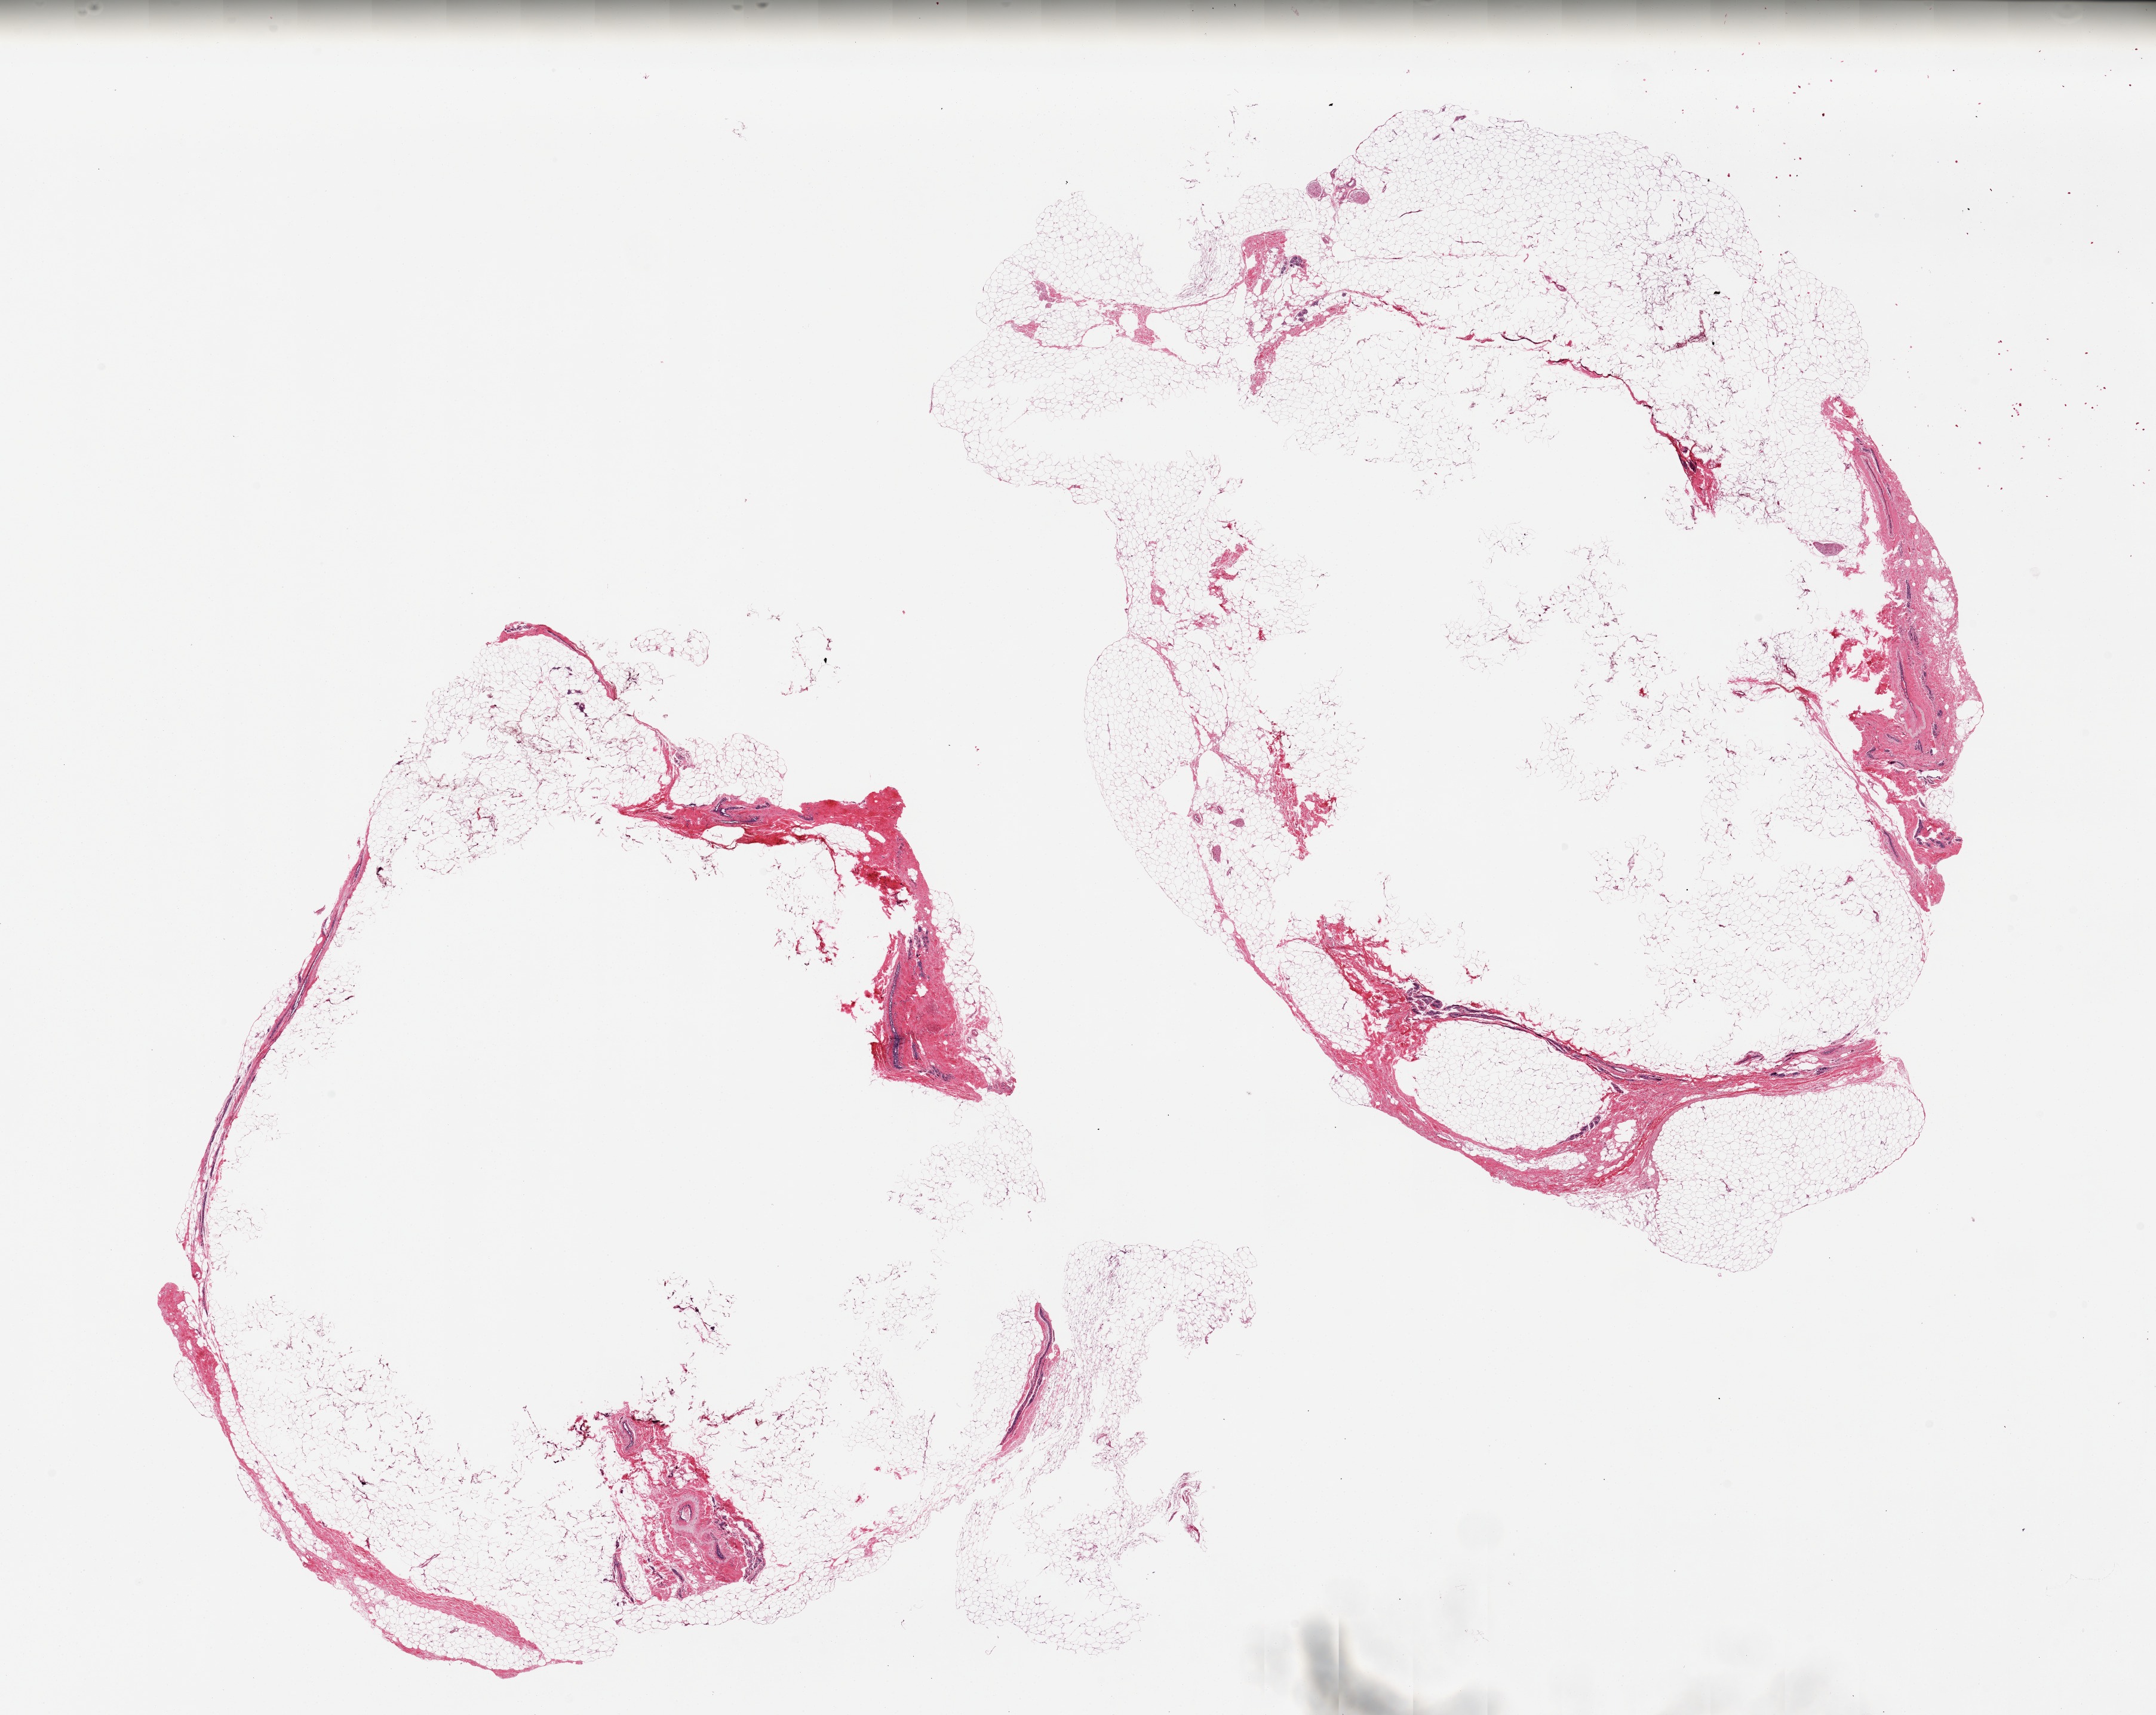
Whole-slide image, haematoxylin and eosin stain — a low-resolution overview of the entire scanned area, about 28.5 x 22.7 mm (slide scanned at 20x); PAXgene-fixed, paraffin-embedded tissue; sampled site (target tissue): breast; tissue donor sample. Female donor.
Review note (as recorded): 2 pieces, 16x13 & 17x12mm; mainly fibroadipose tissue, a few atrophic ductal elements noted.